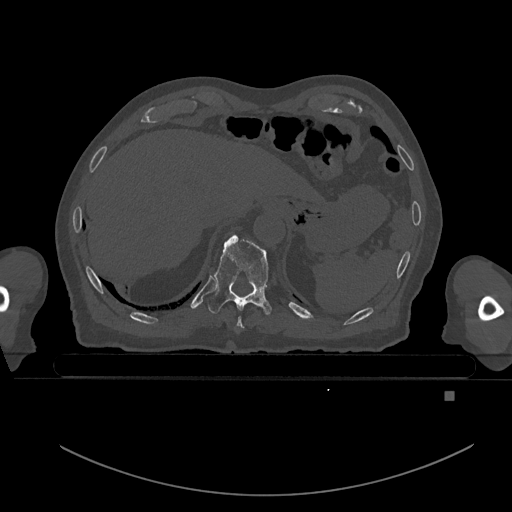
CT including the spine, one axial slice; position 93 of 969 along the scan axis; bone window (W 1800 / L 400 HU); 0.5 mm slice thickness; 512 × 512 image matrix. Male patient, age 82 years. From the clinical record (not read from this slice): primary cancer: prostate; vertebrae with lytic lesions (as recorded): T11, T9, T8, T2.
Outlined on this slice (semi-automatic segmentation, software-assisted and operator-edited):
- T10 vertebra: bounding box [x1, y1, x2, y2] px = [208, 234, 273, 315]
- T9 vertebra: [236, 316, 244, 330]